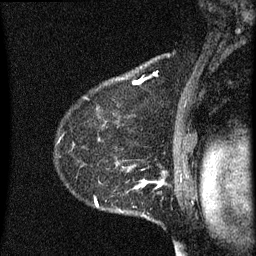
Breast MRI (dynamic contrast-enhanced), one sagittal slice. Slice 48 of 60 in the series (ordered by position). Dynamic contrast-enhanced series, image 2 of 3 at this slice position (ordered by acquisition). 1.5 T. TE 4.2 ms, TR 8 ms. 2 mm slice thickness. 256 × 256 image matrix, field of view 180 × 180 mm. Patient: female, 55 years.
Outlined on this slice (semi-automatic segmentation, software-assisted and operator-edited):
- analysis volume of interest (the breast-tissue region the enhancement analysis was run in; not a lesion): bounding box <55,156,145,217> (left, top, right, bottom; pixels)
- tumour enhancement mask (voxels above the 70 % enhancement threshold inside the analysis volume of interest): <96,170,145,213>